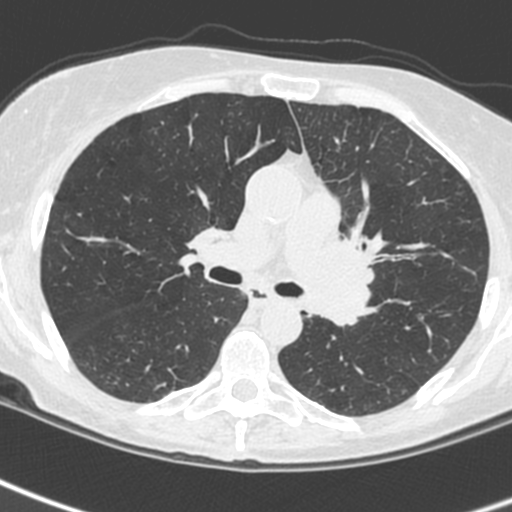
Low-dose screening chest CT, one axial slice; slice 151 of 242 in the series (ordered by position); lung window (W 1500 / L -600 HU); 1.3 mm slice thickness; 512 × 512 image matrix.
Structures marked on this image (manually delineated by an expert):
- lesion 3 (tumor, upper lobe of left lung): bounding box [x1, y1, x2, y2] px = [305, 228, 374, 326]